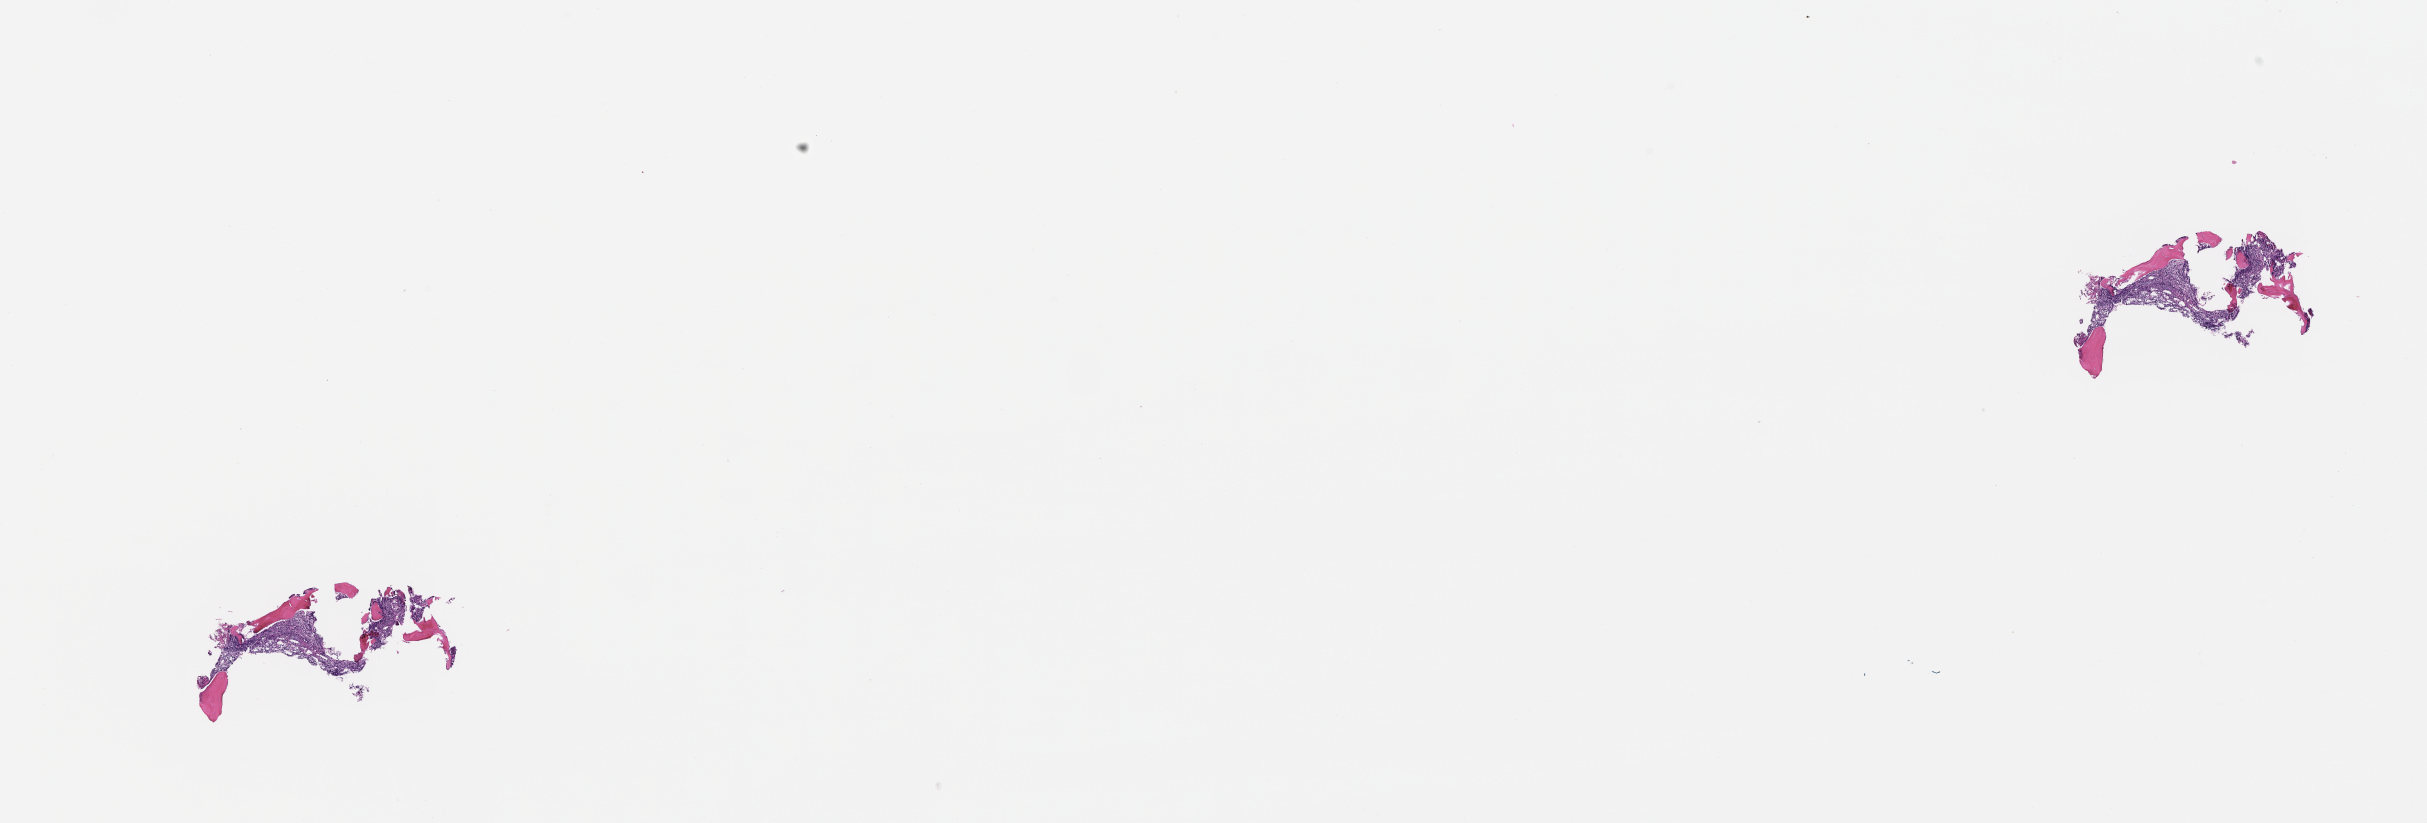
Whole-slide image, haematoxylin and eosin stain, a low-resolution overview of the entire scanned area, about 19.6 x 6.6 mm; formalin-fixed paraffin-embedded section; tissue site: bone marrow; specimen time point: collected at baseline (before treatment). Male patient.
From a patient with: Plasma Cell Myeloma.